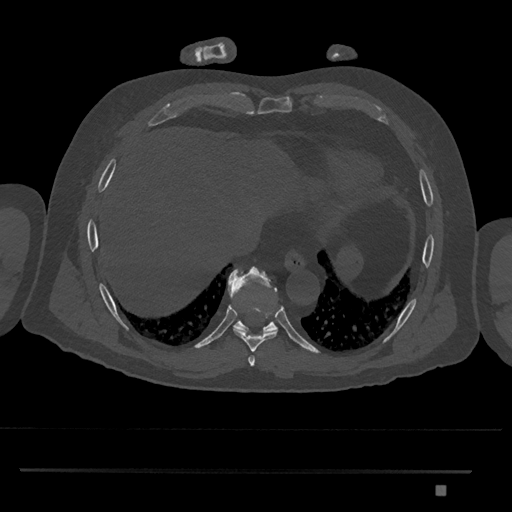
CT including the spine, one axial slice. Position 1088 of 1134 along the scan axis. 120 kVp. Bone window (W 1800 / L 400 HU). 512 × 512 image matrix, field of view 429 × 429 mm. Male patient, age 65 years. From the clinical record (not read from this slice): primary cancer: prostate.
Structures marked on this image (semi-automatic segmentation, software-assisted and operator-edited):
- T8 vertebra: bounding box <234,305,278,352> (left, top, right, bottom; pixels)
- T9 vertebra: <228,266,278,333>